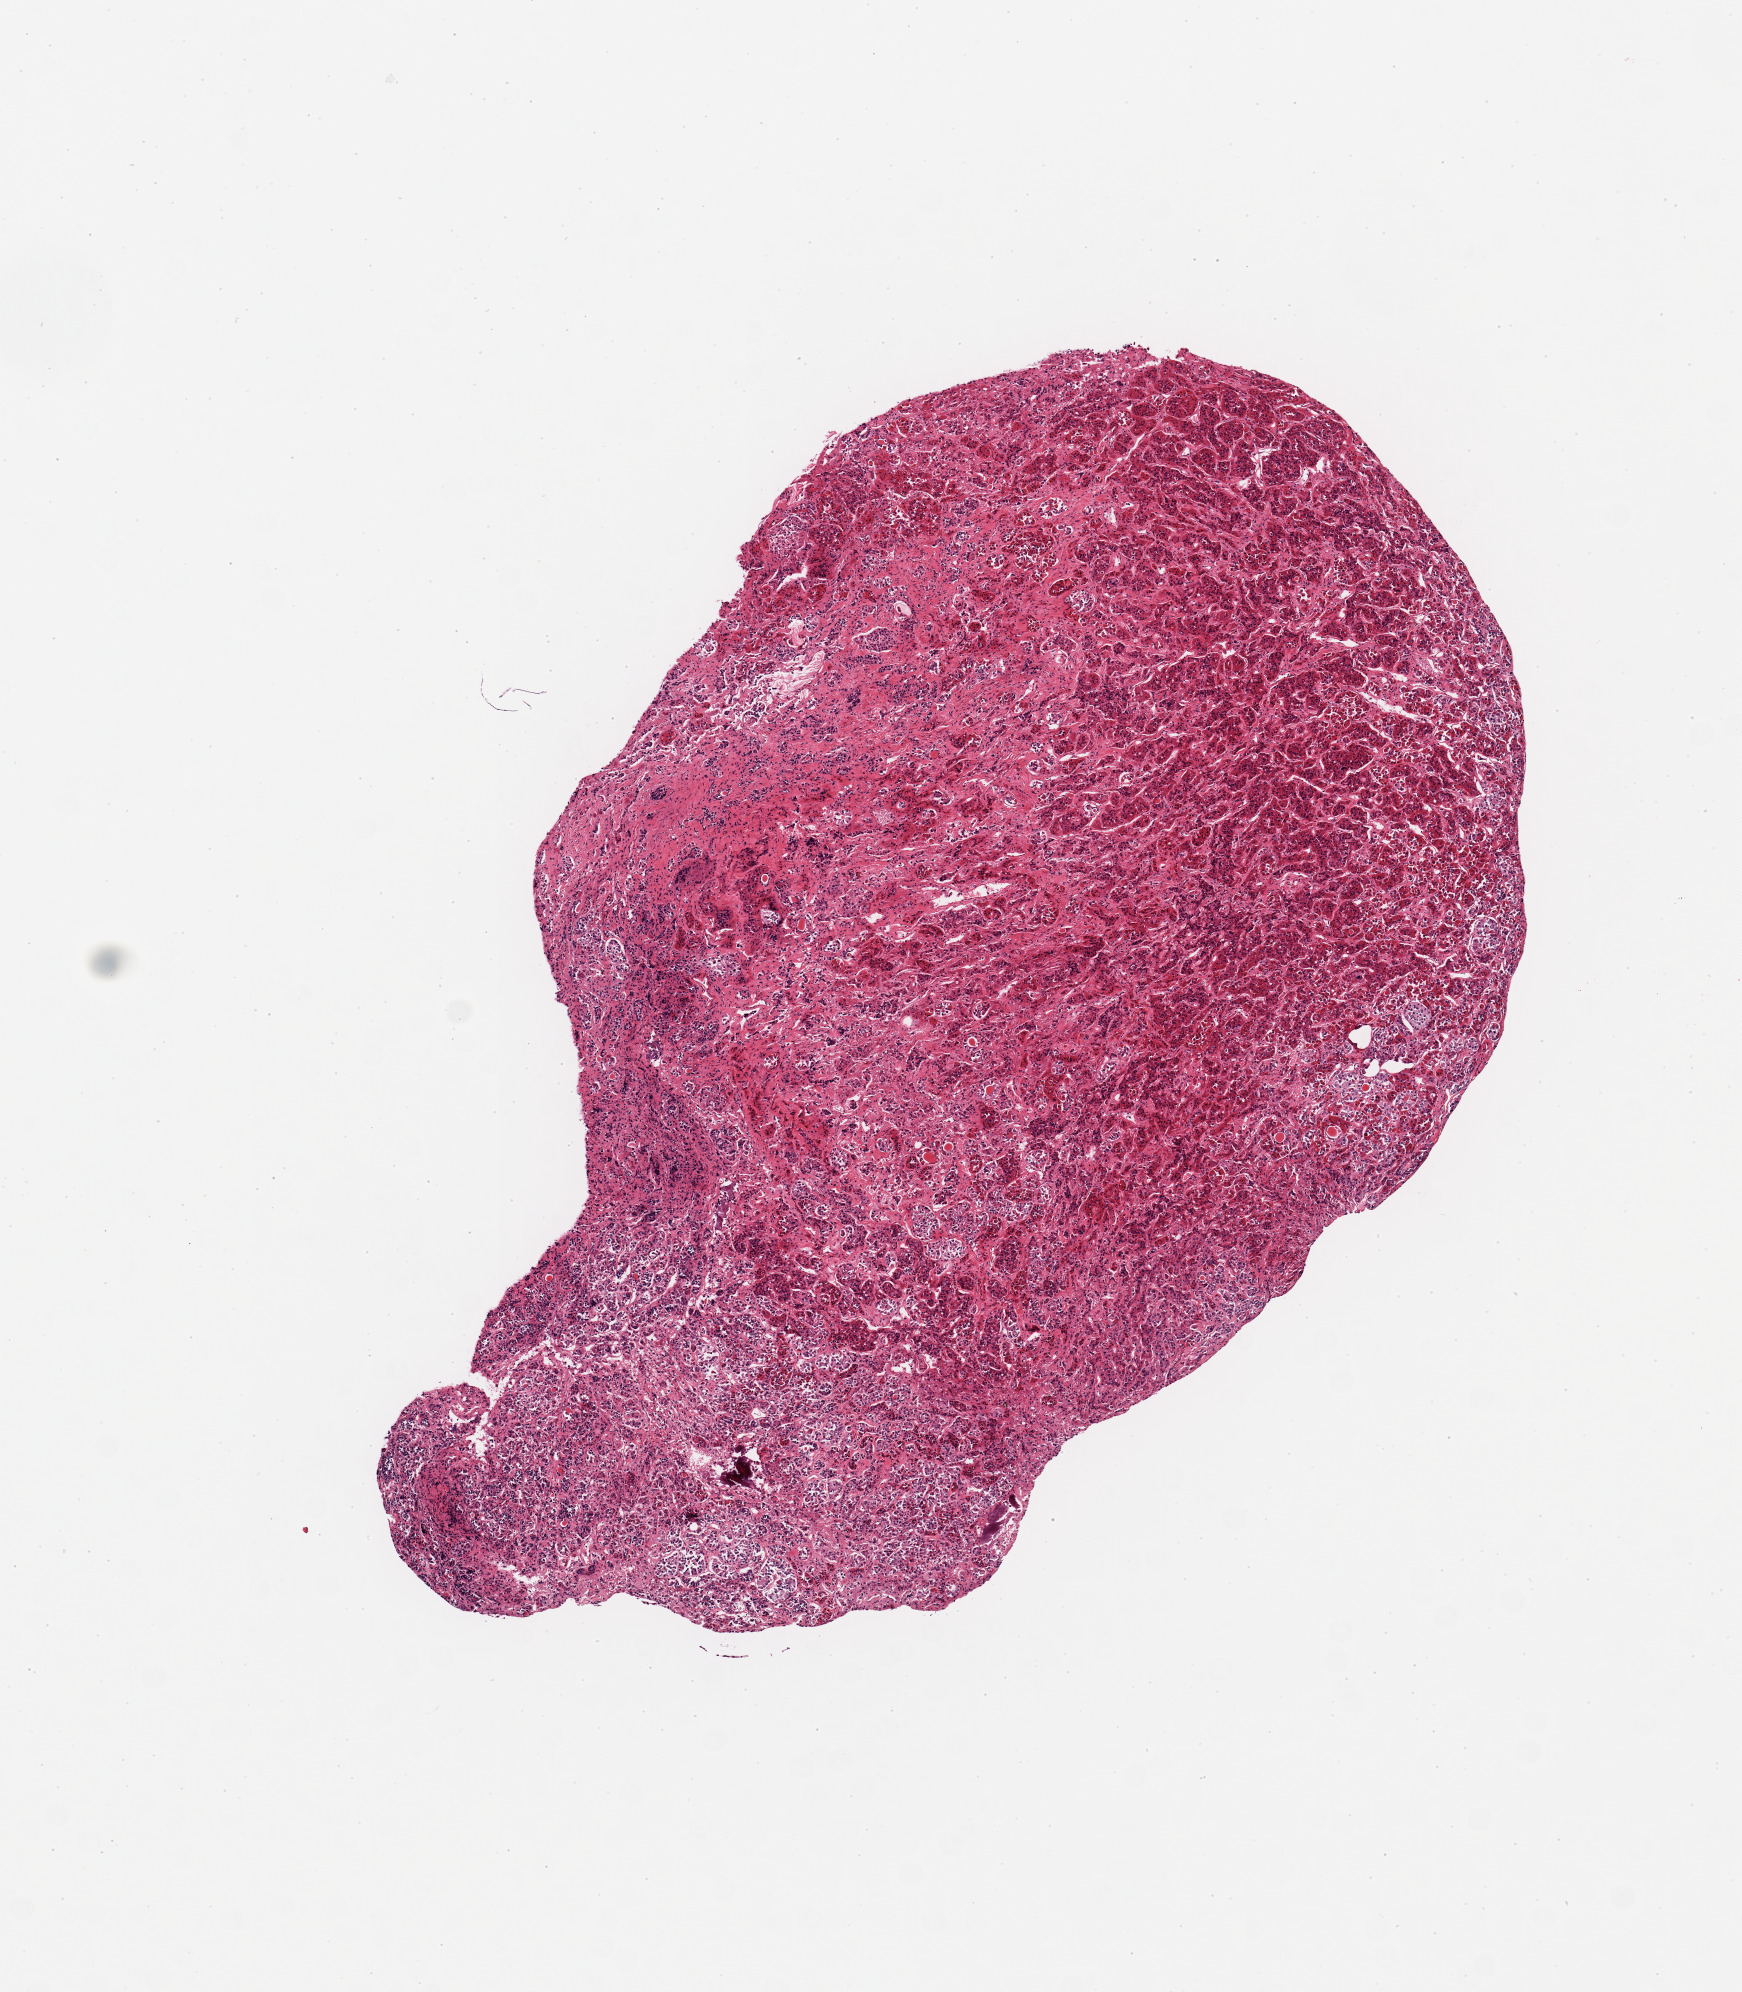
Whole-slide image, hematoxylin and eosin (H&E) stain, whole scanned area (about 6.9 x 7.9 mm) shown as a low-resolution overview; PAXgene-fixed paraffin-embedded (PFPE) section; section of pituitary (target tissue); donor tissue sample. Male donor.
- reviewer comment on this tissue sample: 1 piece; no neural tissue in this cut